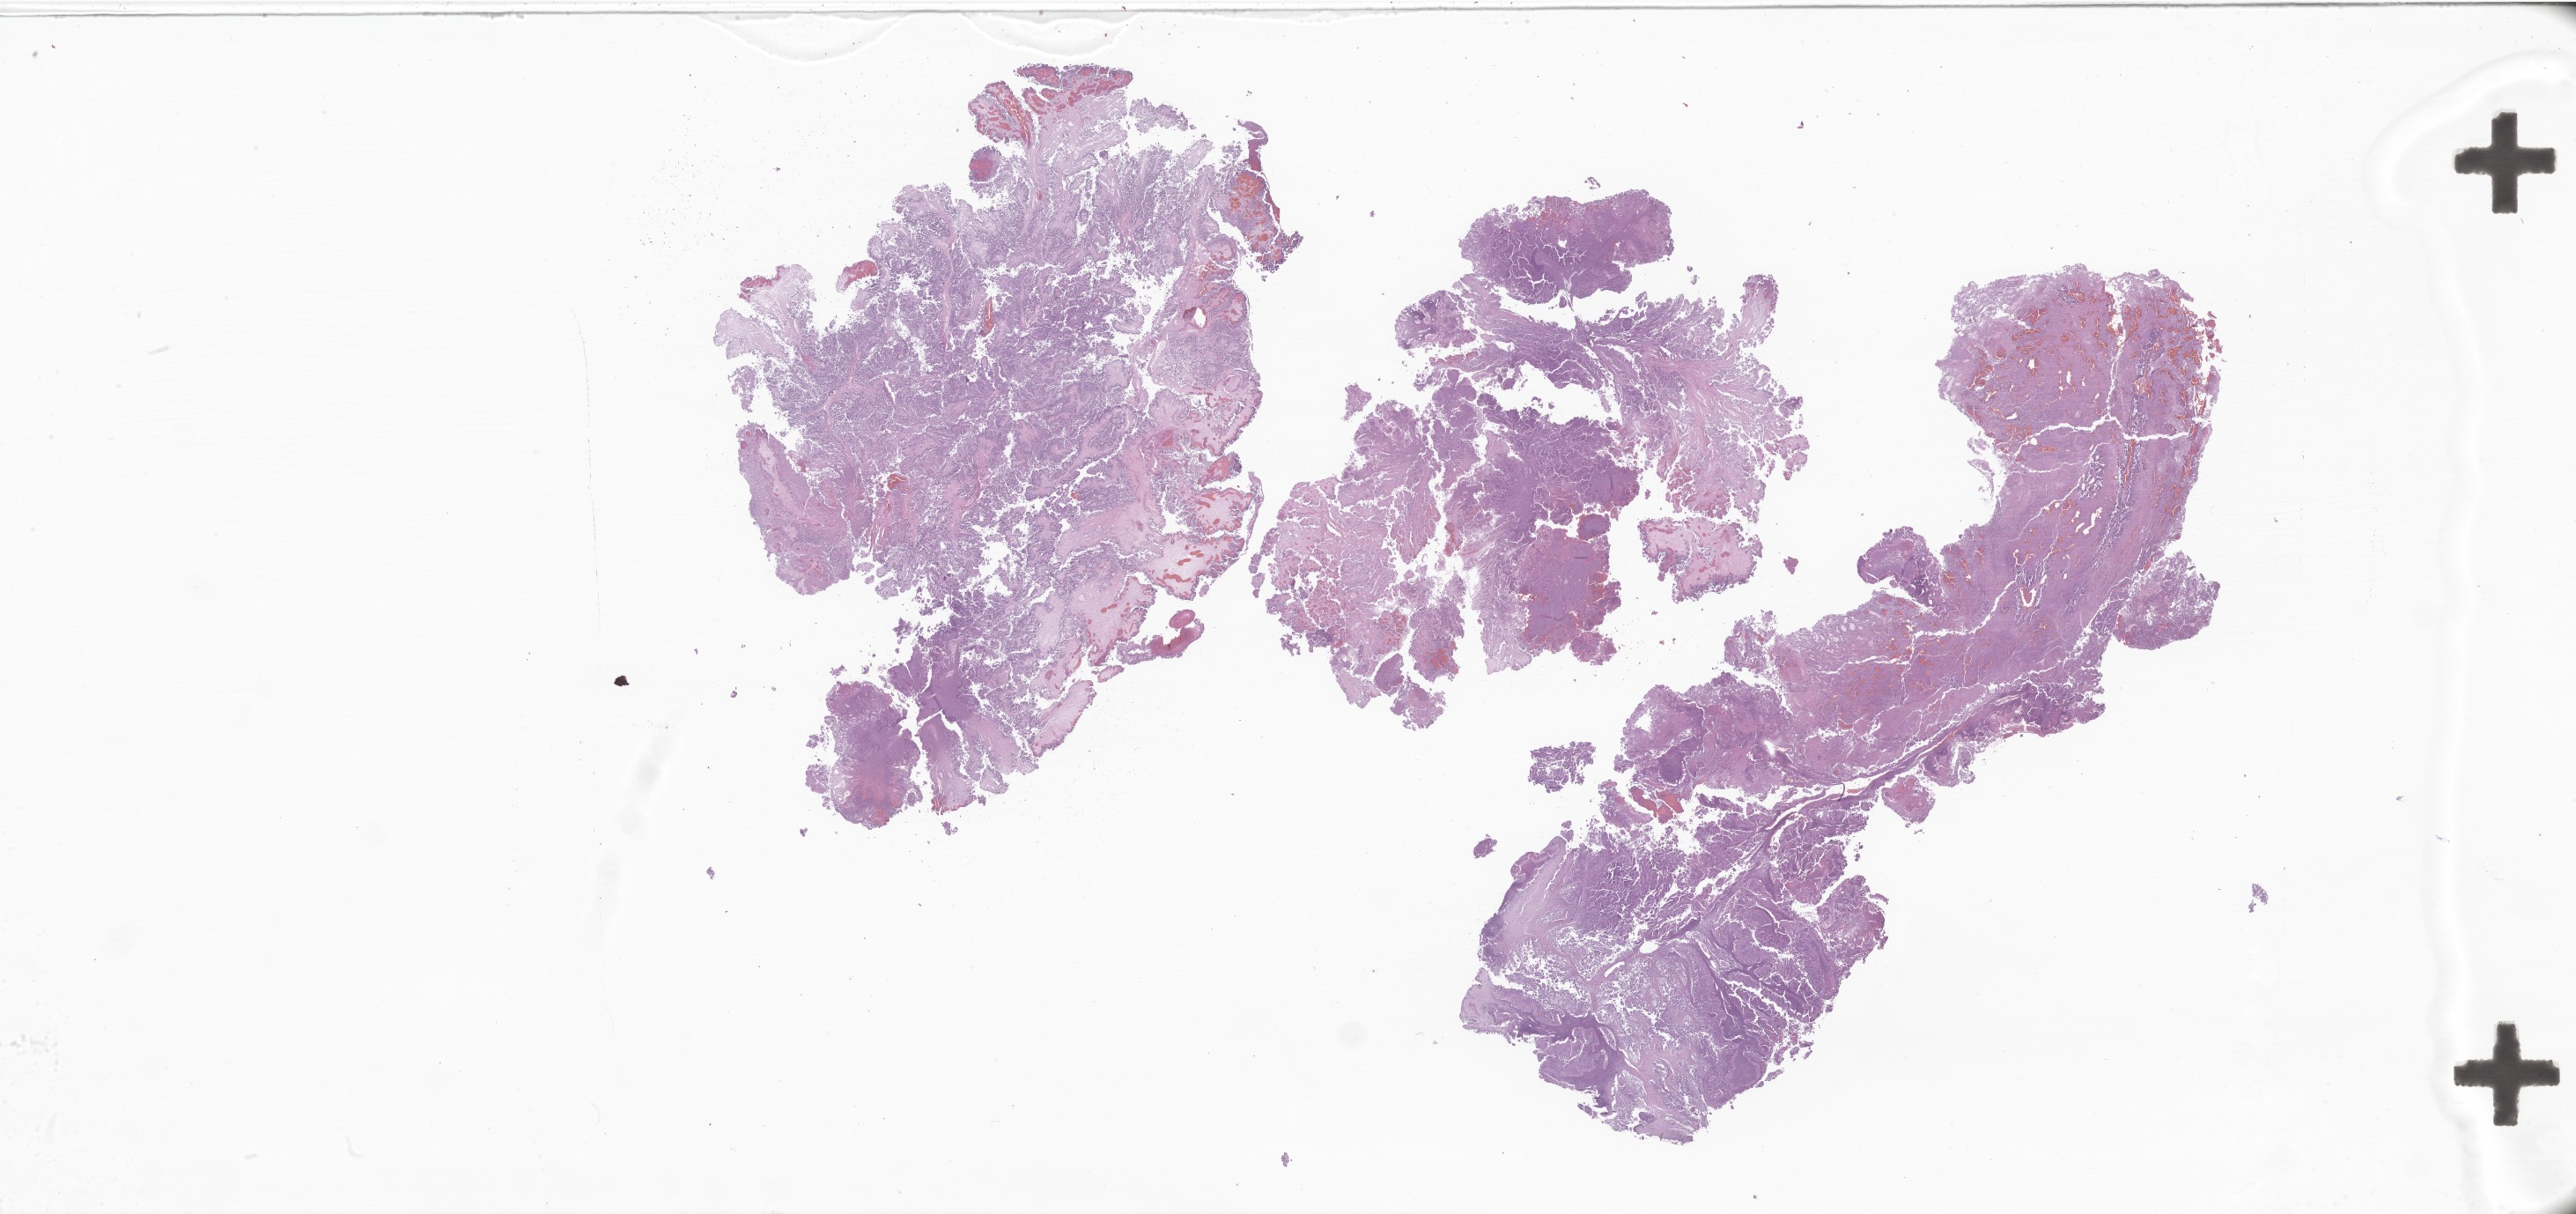
Whole-slide image, H&E stain of tumor tissue from the brain, whole scanned area (about 49.3 x 23.2 mm) shown as a low-resolution overview; formalin-fixed paraffin-embedded section. Patient: female, age 218 days.
Diagnosis (ICD-O-3 morphology term): Choroid plexus papilloma, NOS.